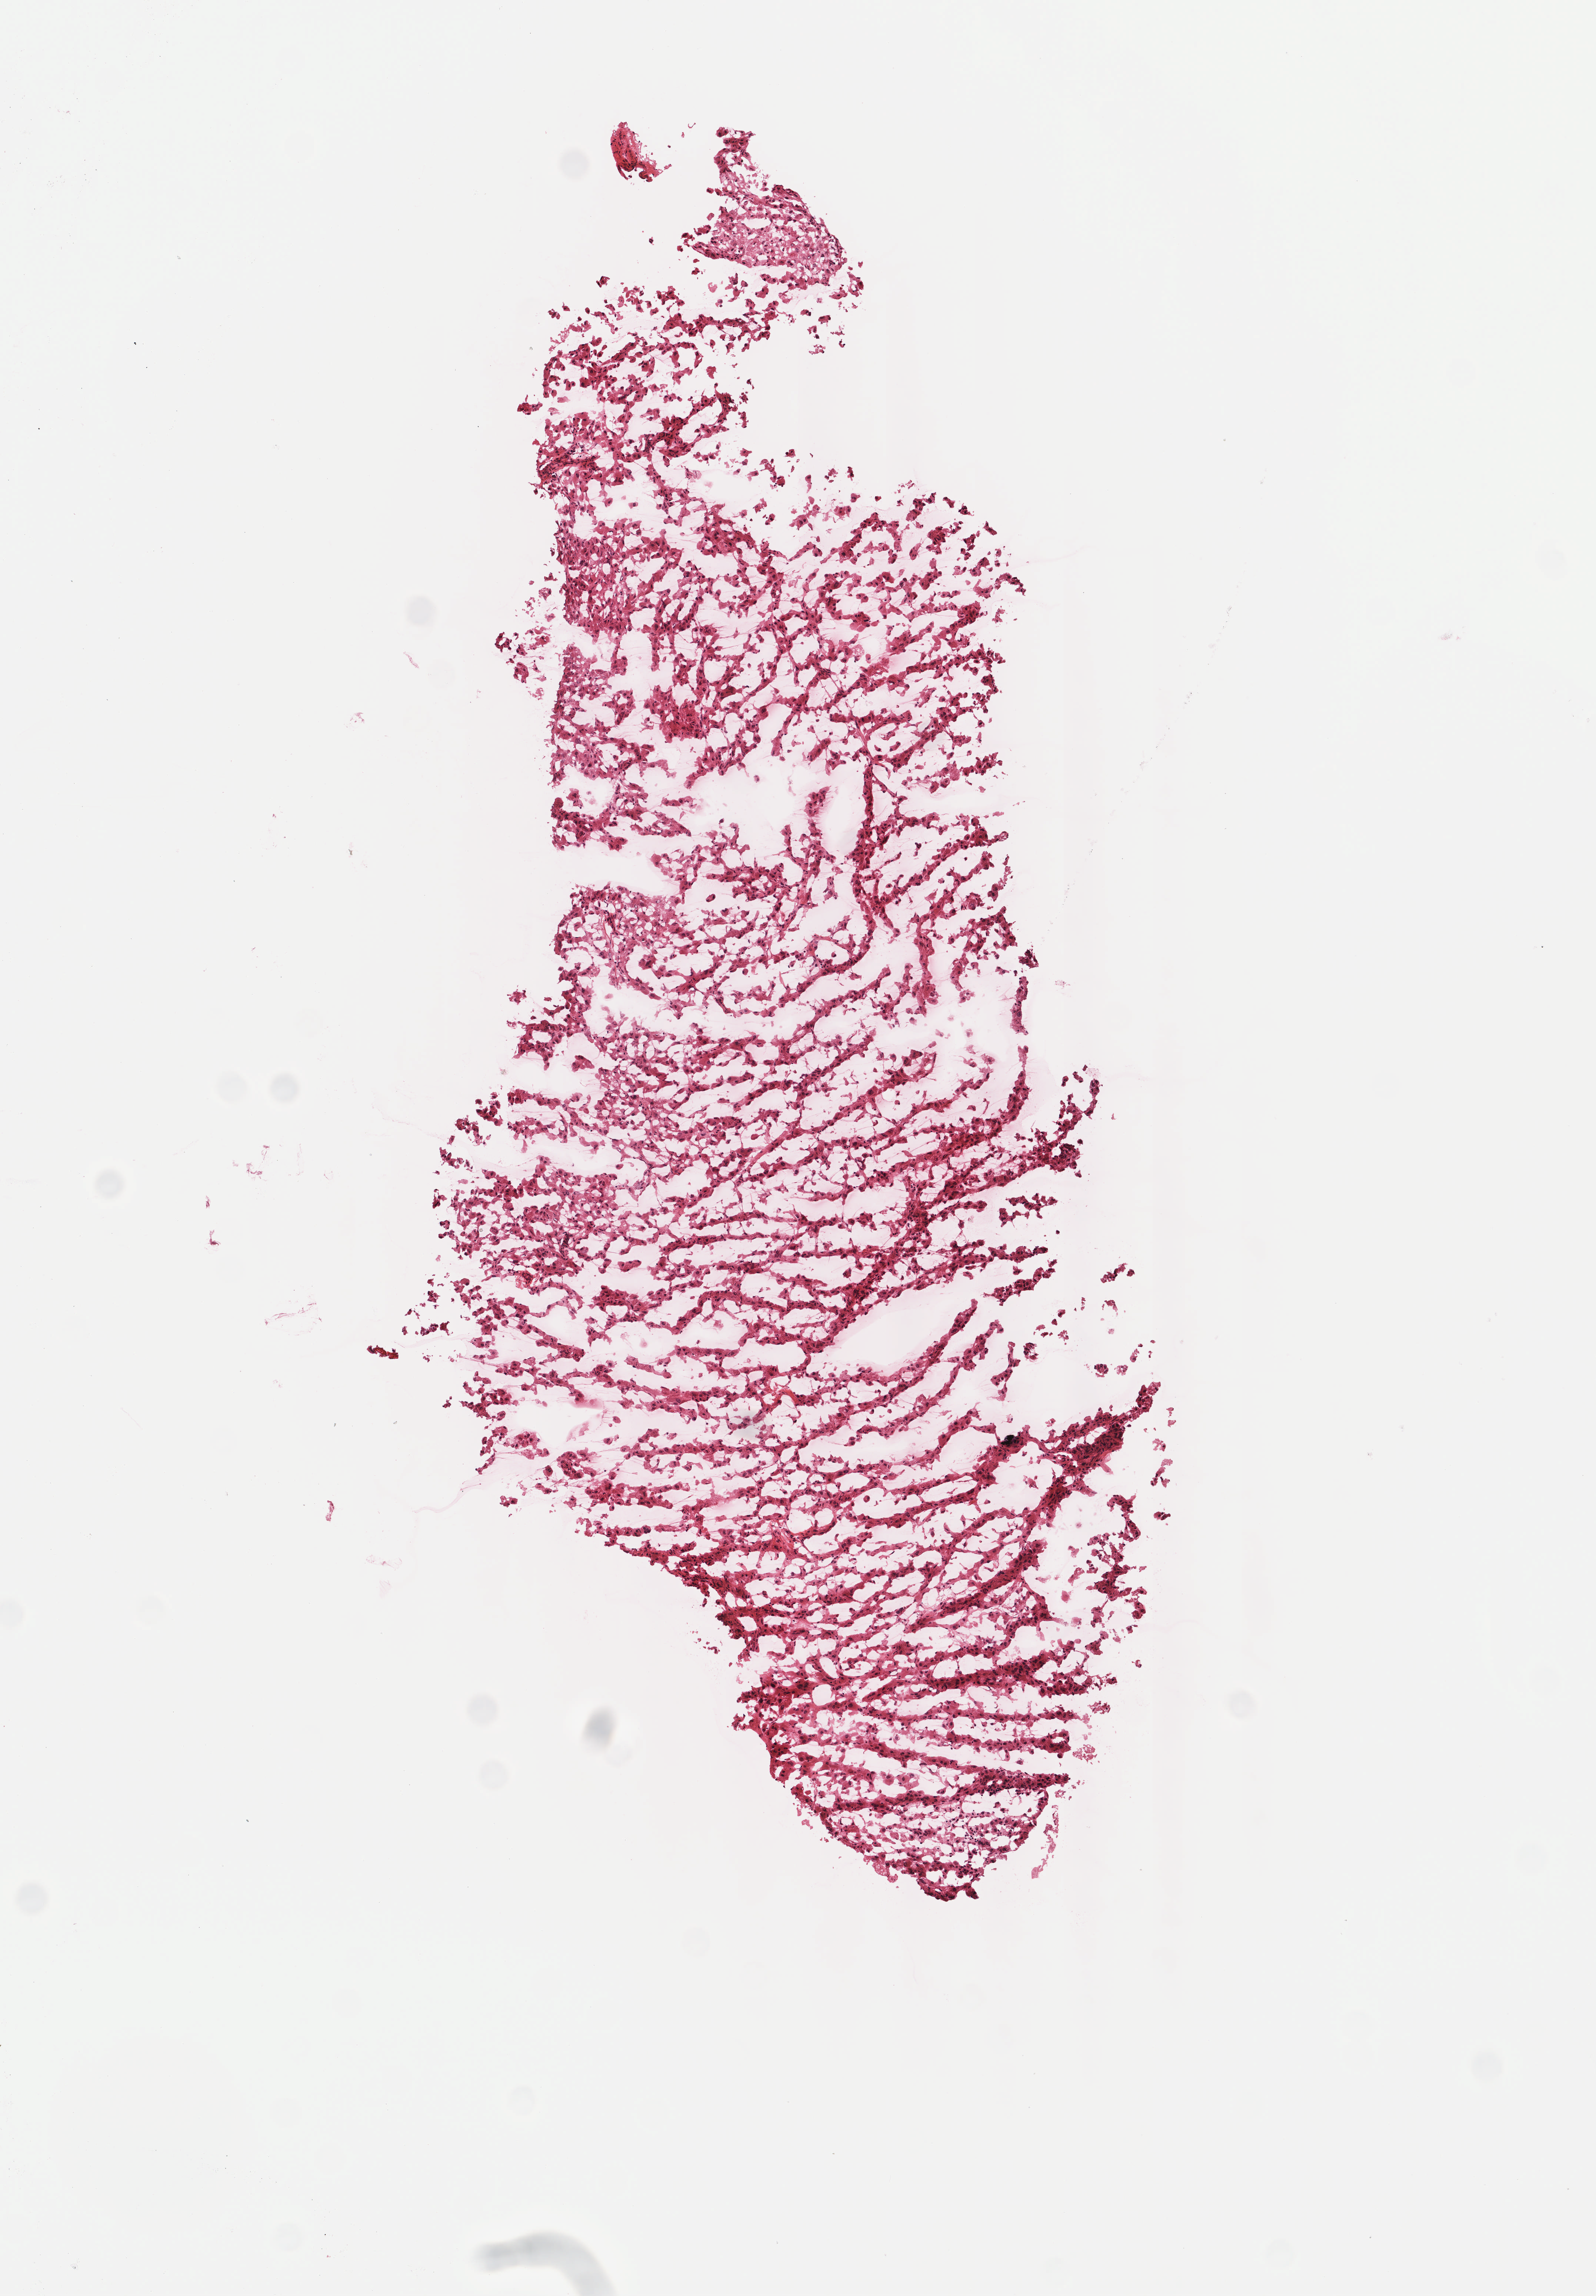
H&E-stained whole-slide image, shown as a low-resolution overview of the whole scanned area (about 4.3 x 6.2 mm); frozen section from the top of the tissue portion; primary tumour sample from the adrenal cortex. Male, age 22 years at initial diagnosis. Pathologist review of this section (percent, as recorded): tumour cells 95%, tumour nuclei 90%, normal cells 0%, stromal cells 5%, necrosis 0%. Inflammatory infiltration, as recorded: lymphocyte infiltration 5%, monocyte infiltration 0%, neutrophil infiltration 0%.
Histologic diagnosis: Adrenal cortical carcinoma (cortex of adrenal gland).